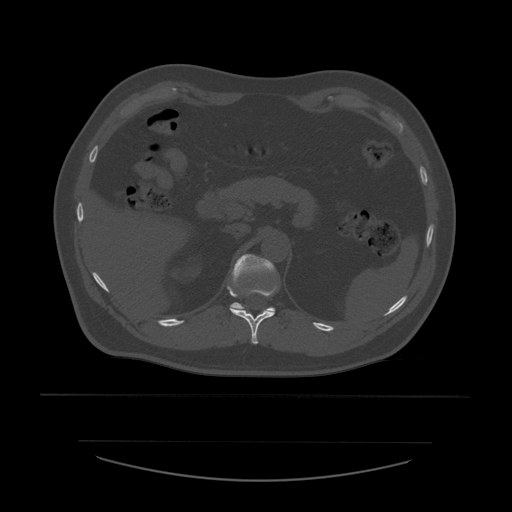
CT including the spine, one axial slice; 120 kVp; bone window (W 1800 / L 400 HU); 1.25 mm slice thickness; 512 × 512 image matrix, field of view 441 × 441 mm. Patient age 44 years. From the clinical record (not read from this slice): primary cancer: soft tissue sarcoma.
Structures marked on this image (semi-automatically segmented with operator editing):
- T11 vertebra: bounding box (x1, y1, x2, y2) in pixels: (230, 286, 278, 345)
- T12 vertebra: (227, 254, 276, 312)